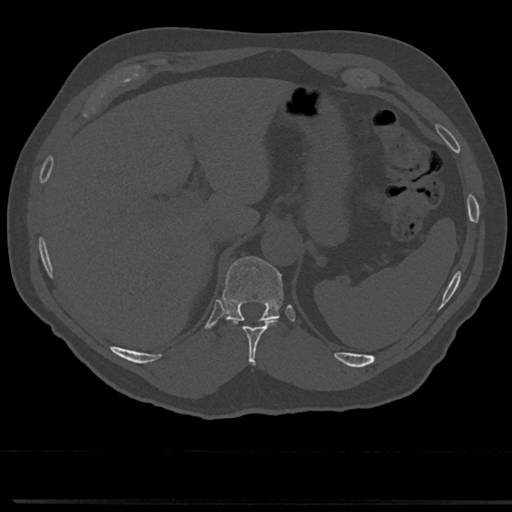
CT including the spine, one axial slice. Position 227 of 817 along the scan axis. Reconstruction kernel Br40s/3. Bone window (W 1800 / L 400 HU). 0.5 mm slice thickness. 512 × 512 image matrix, field of view 355 × 355 mm. Male patient, age 61 years. From the clinical record (not read from this slice): primary cancer: prostate.
Annotated regions visible in this slice (semi-automatically segmented with operator editing):
- T10 vertebra: bounding box <228,318,280,356> (left, top, right, bottom; pixels)
- T11 vertebra: <223,256,283,322>